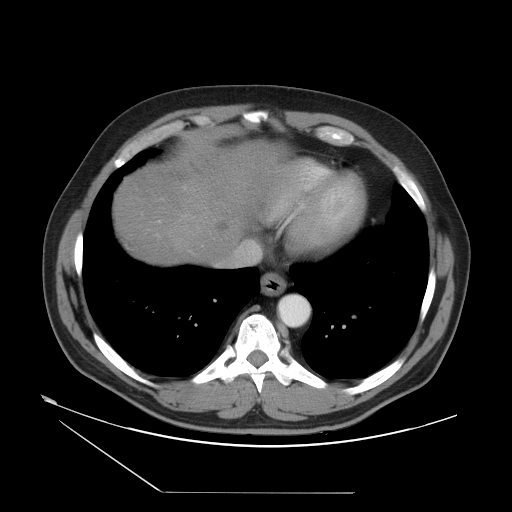
Contrast-enhanced abdominal CT, one axial slice. Position 47 of 55 along the scan axis. Reconstruction kernel STANDARD. Intravenous contrast given. Soft-tissue window (W 400 / L 40 HU). 512 × 512 image matrix, field of view 454 × 454 mm. Male patient, age 59 years. Case-level facts recorded for this patient, not image findings: diagnosis: colorectal cancer liver metastases, imaged before liver resection; multiple liver metastases: yes; largest metastasis: 0.3 cm.
Structures marked on this image (outlined manually by an expert reader):
- hepatic veins: bounding box (x1, y1, x2, y2) in pixels: (217, 182, 316, 266)
- liver: (115, 147, 285, 263)
- planned liver remnant (the part of the liver to remain after resection): (115, 174, 223, 263)
- portal vein (with intrahepatic branches): (157, 221, 160, 223)
- liver metastasis: (219, 224, 230, 233)